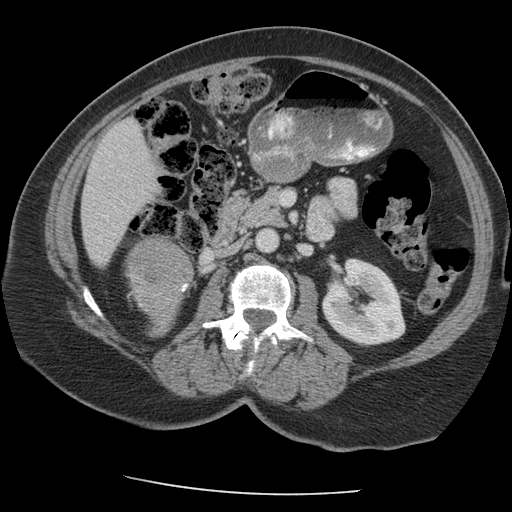
Contrast-enhanced abdominal CT, one axial slice; position 107 of 163 along the scan axis; soft-tissue window (W 400 / L 40 HU); 2.5 mm slice thickness; 512 × 512 image matrix, field of view 360 × 360 mm. Female patient, age 70 years. From the clinical record (not read from this slice): diagnosis: adrenocortical carcinoma; tumour side: right adrenal; tumour size at pathology: 9.5 cm; Ki-67 index: 5 %; stage (as recorded): 2.
Annotated regions visible in this slice (semi-automatically segmented with operator editing):
- mass: box from (x=129, y=239) to (x=191, y=336) px